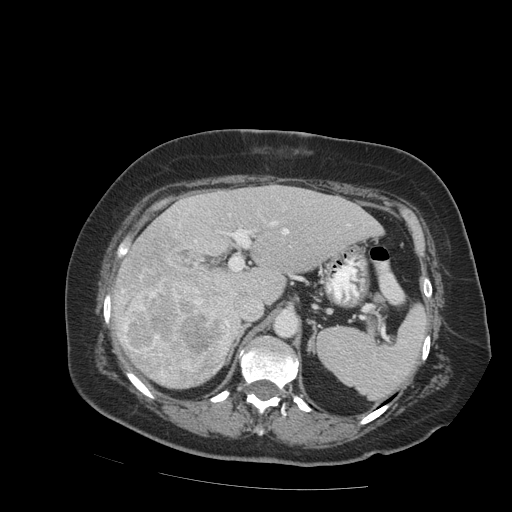
Contrast-enhanced abdominal CT (liver protocol), one axial slice; position 53 of 99 along the scan axis; reconstruction kernel STANDARD; 140 kVp; soft-tissue window (W 400 / L 40 HU); 512 × 512 image matrix, field of view 400 × 400 mm. From the clinical record (not read from this slice): diagnosis: hepatocellular carcinoma (patient treated with transarterial chemoembolisation; whether this scan precedes or follows treatment is not stated here); TNM stage (as recorded): Stage-IVB.
Structures marked on this image (semi-automatic segmentation, software-assisted and operator-edited):
- liver parenchyma outside the tumour (the mass and vessels are separate outlines, so this box may not span the whole liver): bounding box [x1, y1, x2, y2] px = [112, 184, 382, 388]
- mass: [113, 223, 234, 387]
- liver vessels: [179, 222, 349, 247]